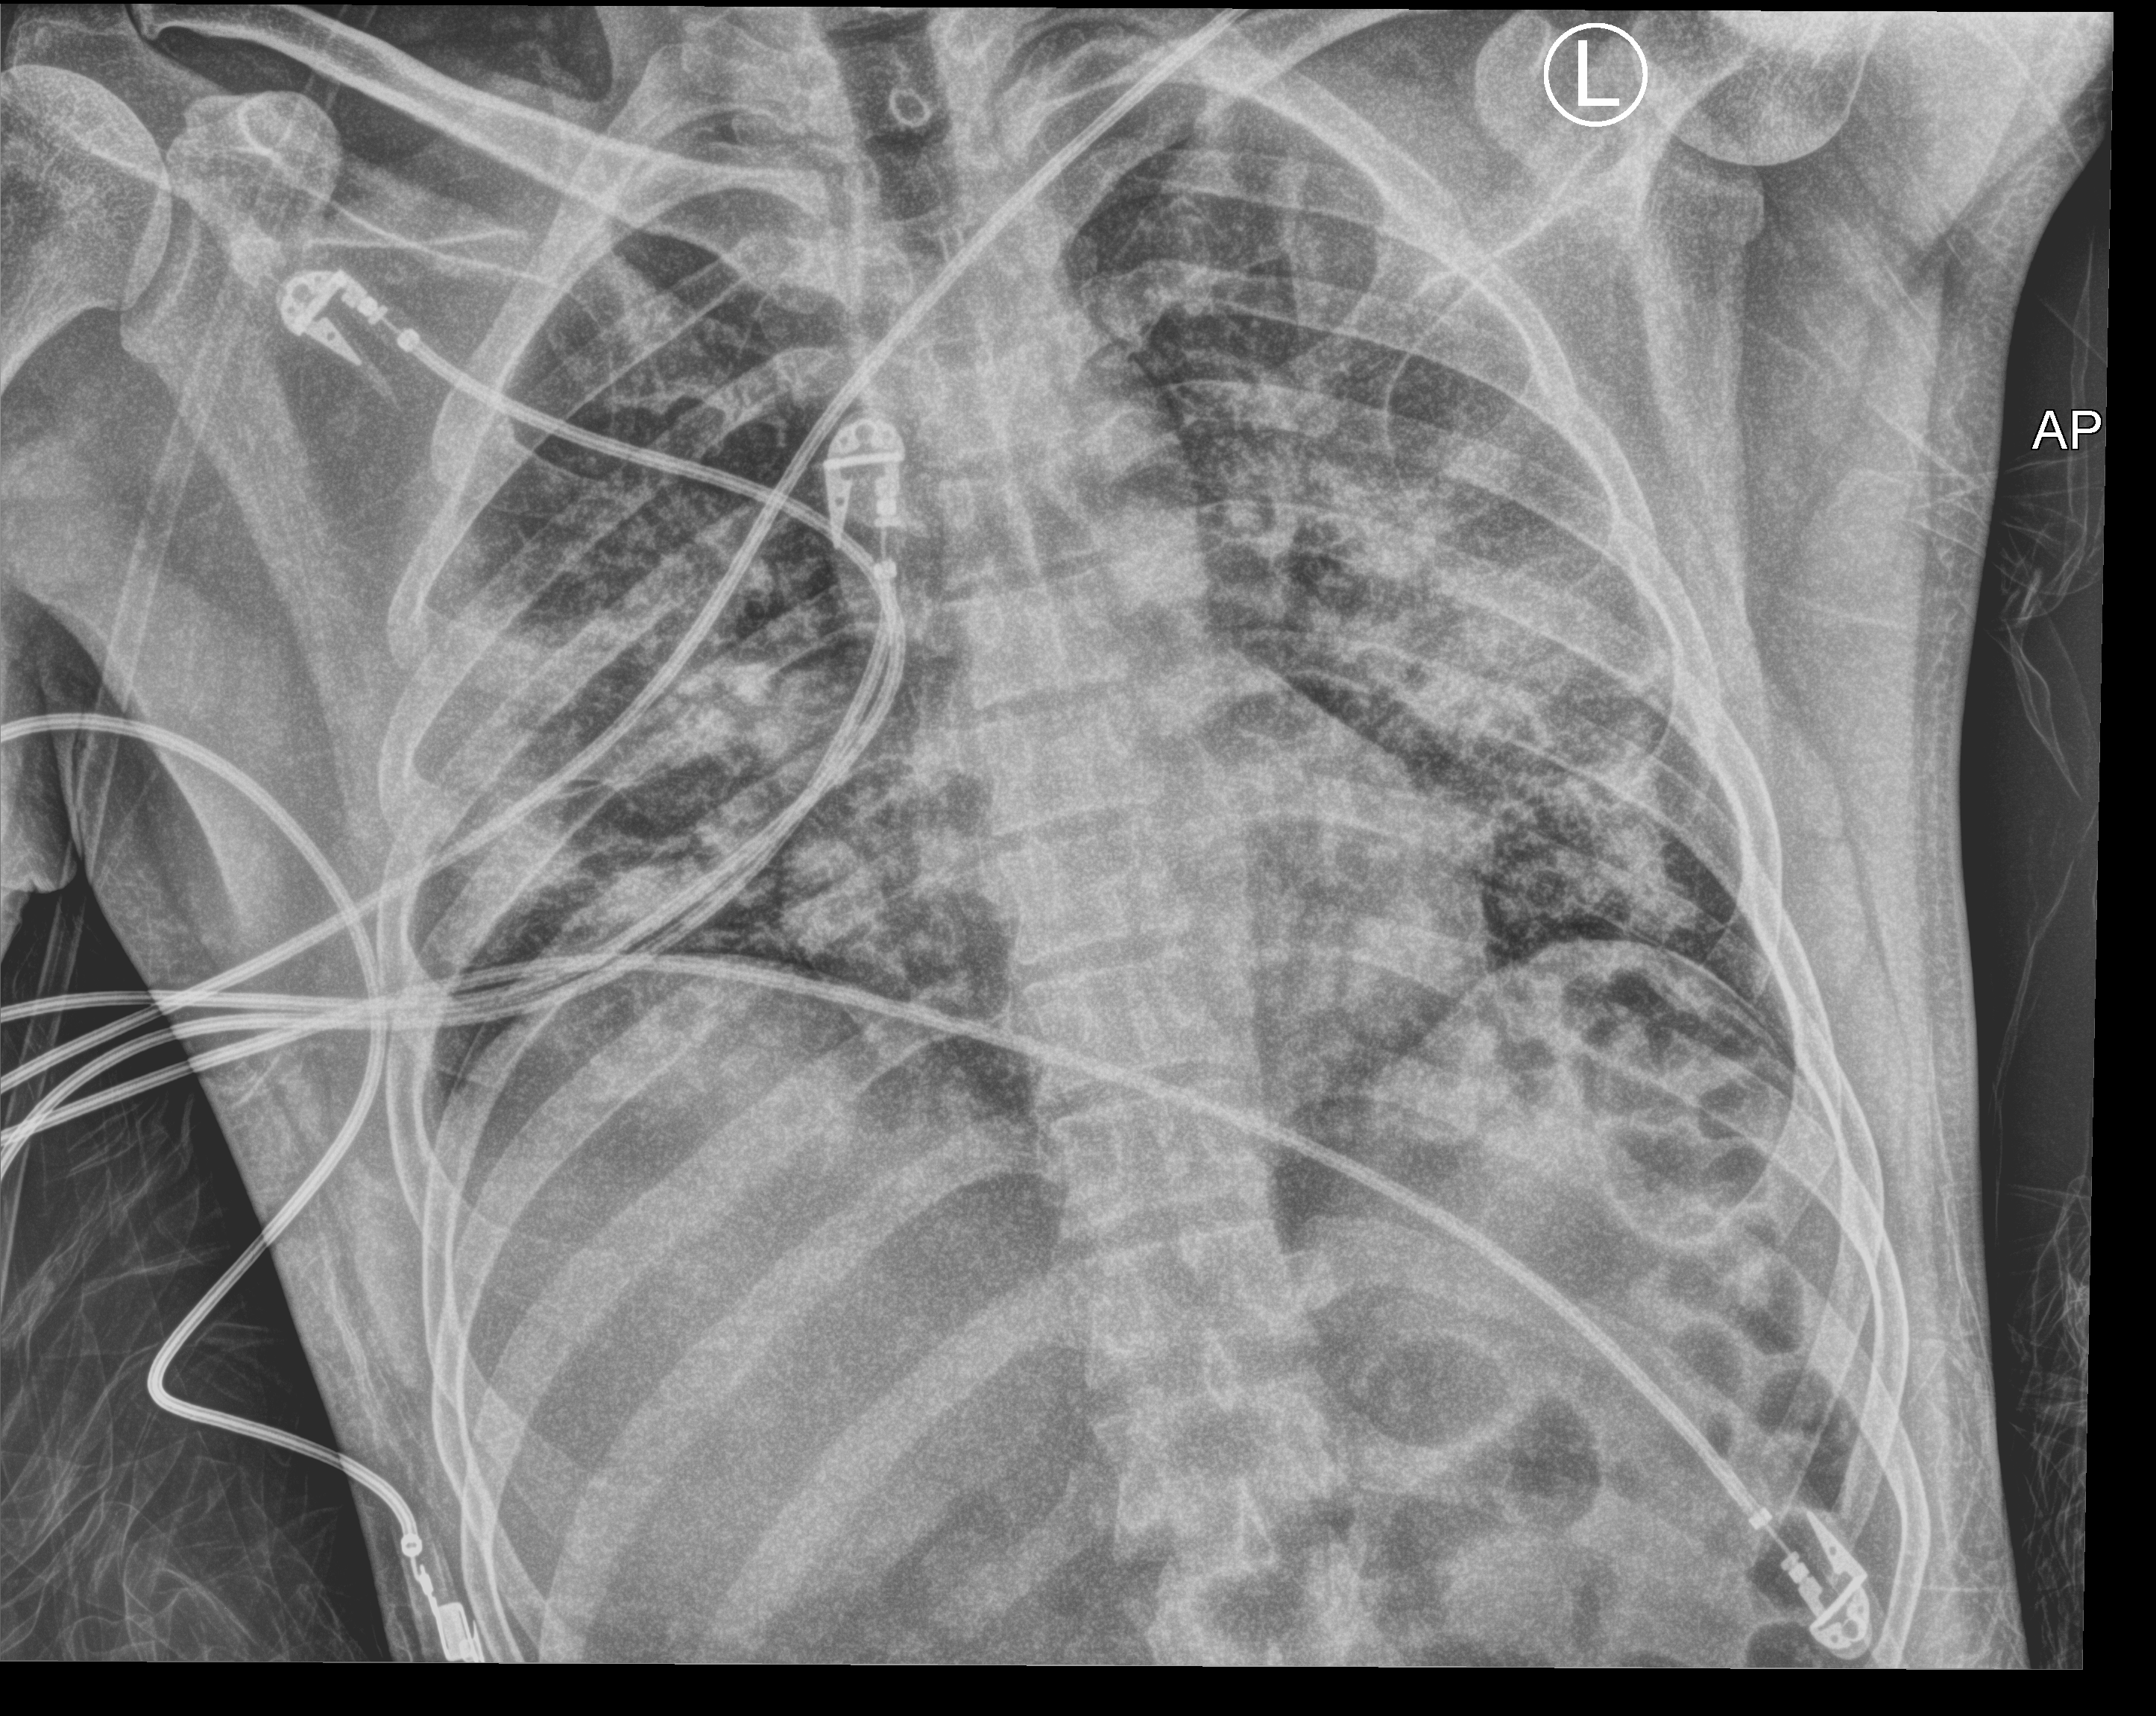
Portable chest radiograph. Male patient hospitalised with COVID-19, age 18–59 years.
From the hospital-stay record, not from the radiograph (when in the stay this image was taken is not recorded):
- mechanically ventilated during this hospital stay: no